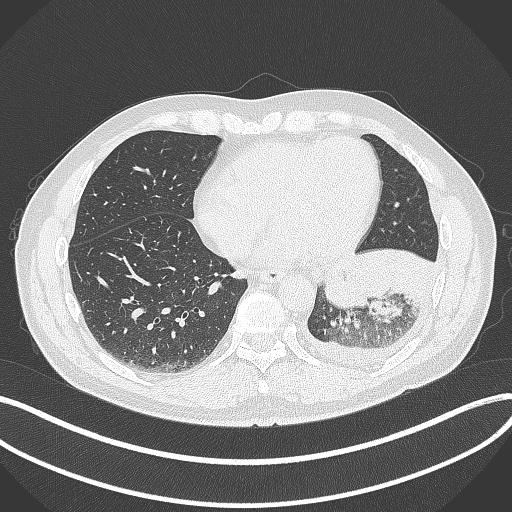
Chest CT, one axial slice; slice 116 of 342 in the series (ordered by position); reconstruction kernel B70f; 120 kVp; lung window (W 1500 / L -600 HU); 1 mm slice thickness; 512 × 512 image matrix, field of view 400 × 400 mm. Male patient, age 58 years. From the clinical record (not read from this slice): clinical TNM (as recorded): T3 N1 M1b.
Annotated regions visible in this slice (rectangle marked by the reading radiologist):
- lung tumour (recorded histology: small cell carcinoma): bounding box <319,248,376,314> (left, top, right, bottom; pixels)